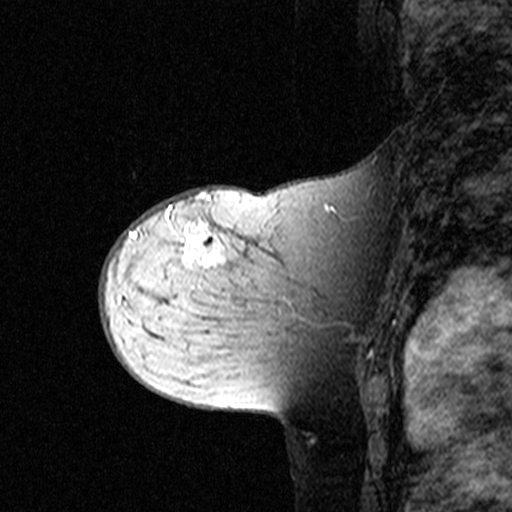
Breast MRI (dynamic contrast-enhanced), one sagittal slice; position 27 of 44 along the scan axis; dynamic contrast-enhanced study with each time point stored as its own series, time point 2 of 3 at this slice position (early post-contrast, ordered by acquisition time); 1.5 T; TE 4.5 ms, TR 11 ms; 3 mm slice thickness; 512 × 512 image matrix, field of view 200 × 200 mm. Patient: female, 44 years. Case-level facts recorded for this patient, not image findings: setting: breast cancer imaged before/during neoadjuvant chemotherapy; receptor status: triple-negative.
Structures marked on this image (semi-automatic segmentation, software-assisted and operator-edited):
- analysis volume of interest (the breast-tissue region the enhancement analysis was run in; not a lesion): box from (x=142, y=208) to (x=349, y=363) px
- tumour enhancement mask (voxels above the 90 % enhancement threshold inside the analysis volume of interest): (x=171, y=208)–(x=226, y=265)